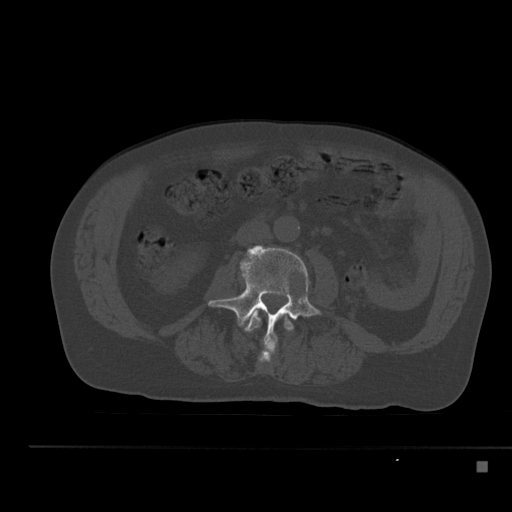
CT including the spine, one axial slice. Slice 167 of 517 in the series (ordered by position). Reconstruction kernel Br40s. 120 kVp. Bone window (W 1800 / L 400 HU). 1.5 mm slice thickness. 512 × 512 image matrix, field of view 408 × 408 mm. Male patient, age 70 years. From the clinical record (not read from this slice): primary cancer: renal.
Outlined on this slice (semi-automatically segmented with operator editing):
- L2 vertebra: box from (x=243, y=310) to (x=294, y=363) px
- L3 vertebra: (x=208, y=245)–(x=322, y=358)